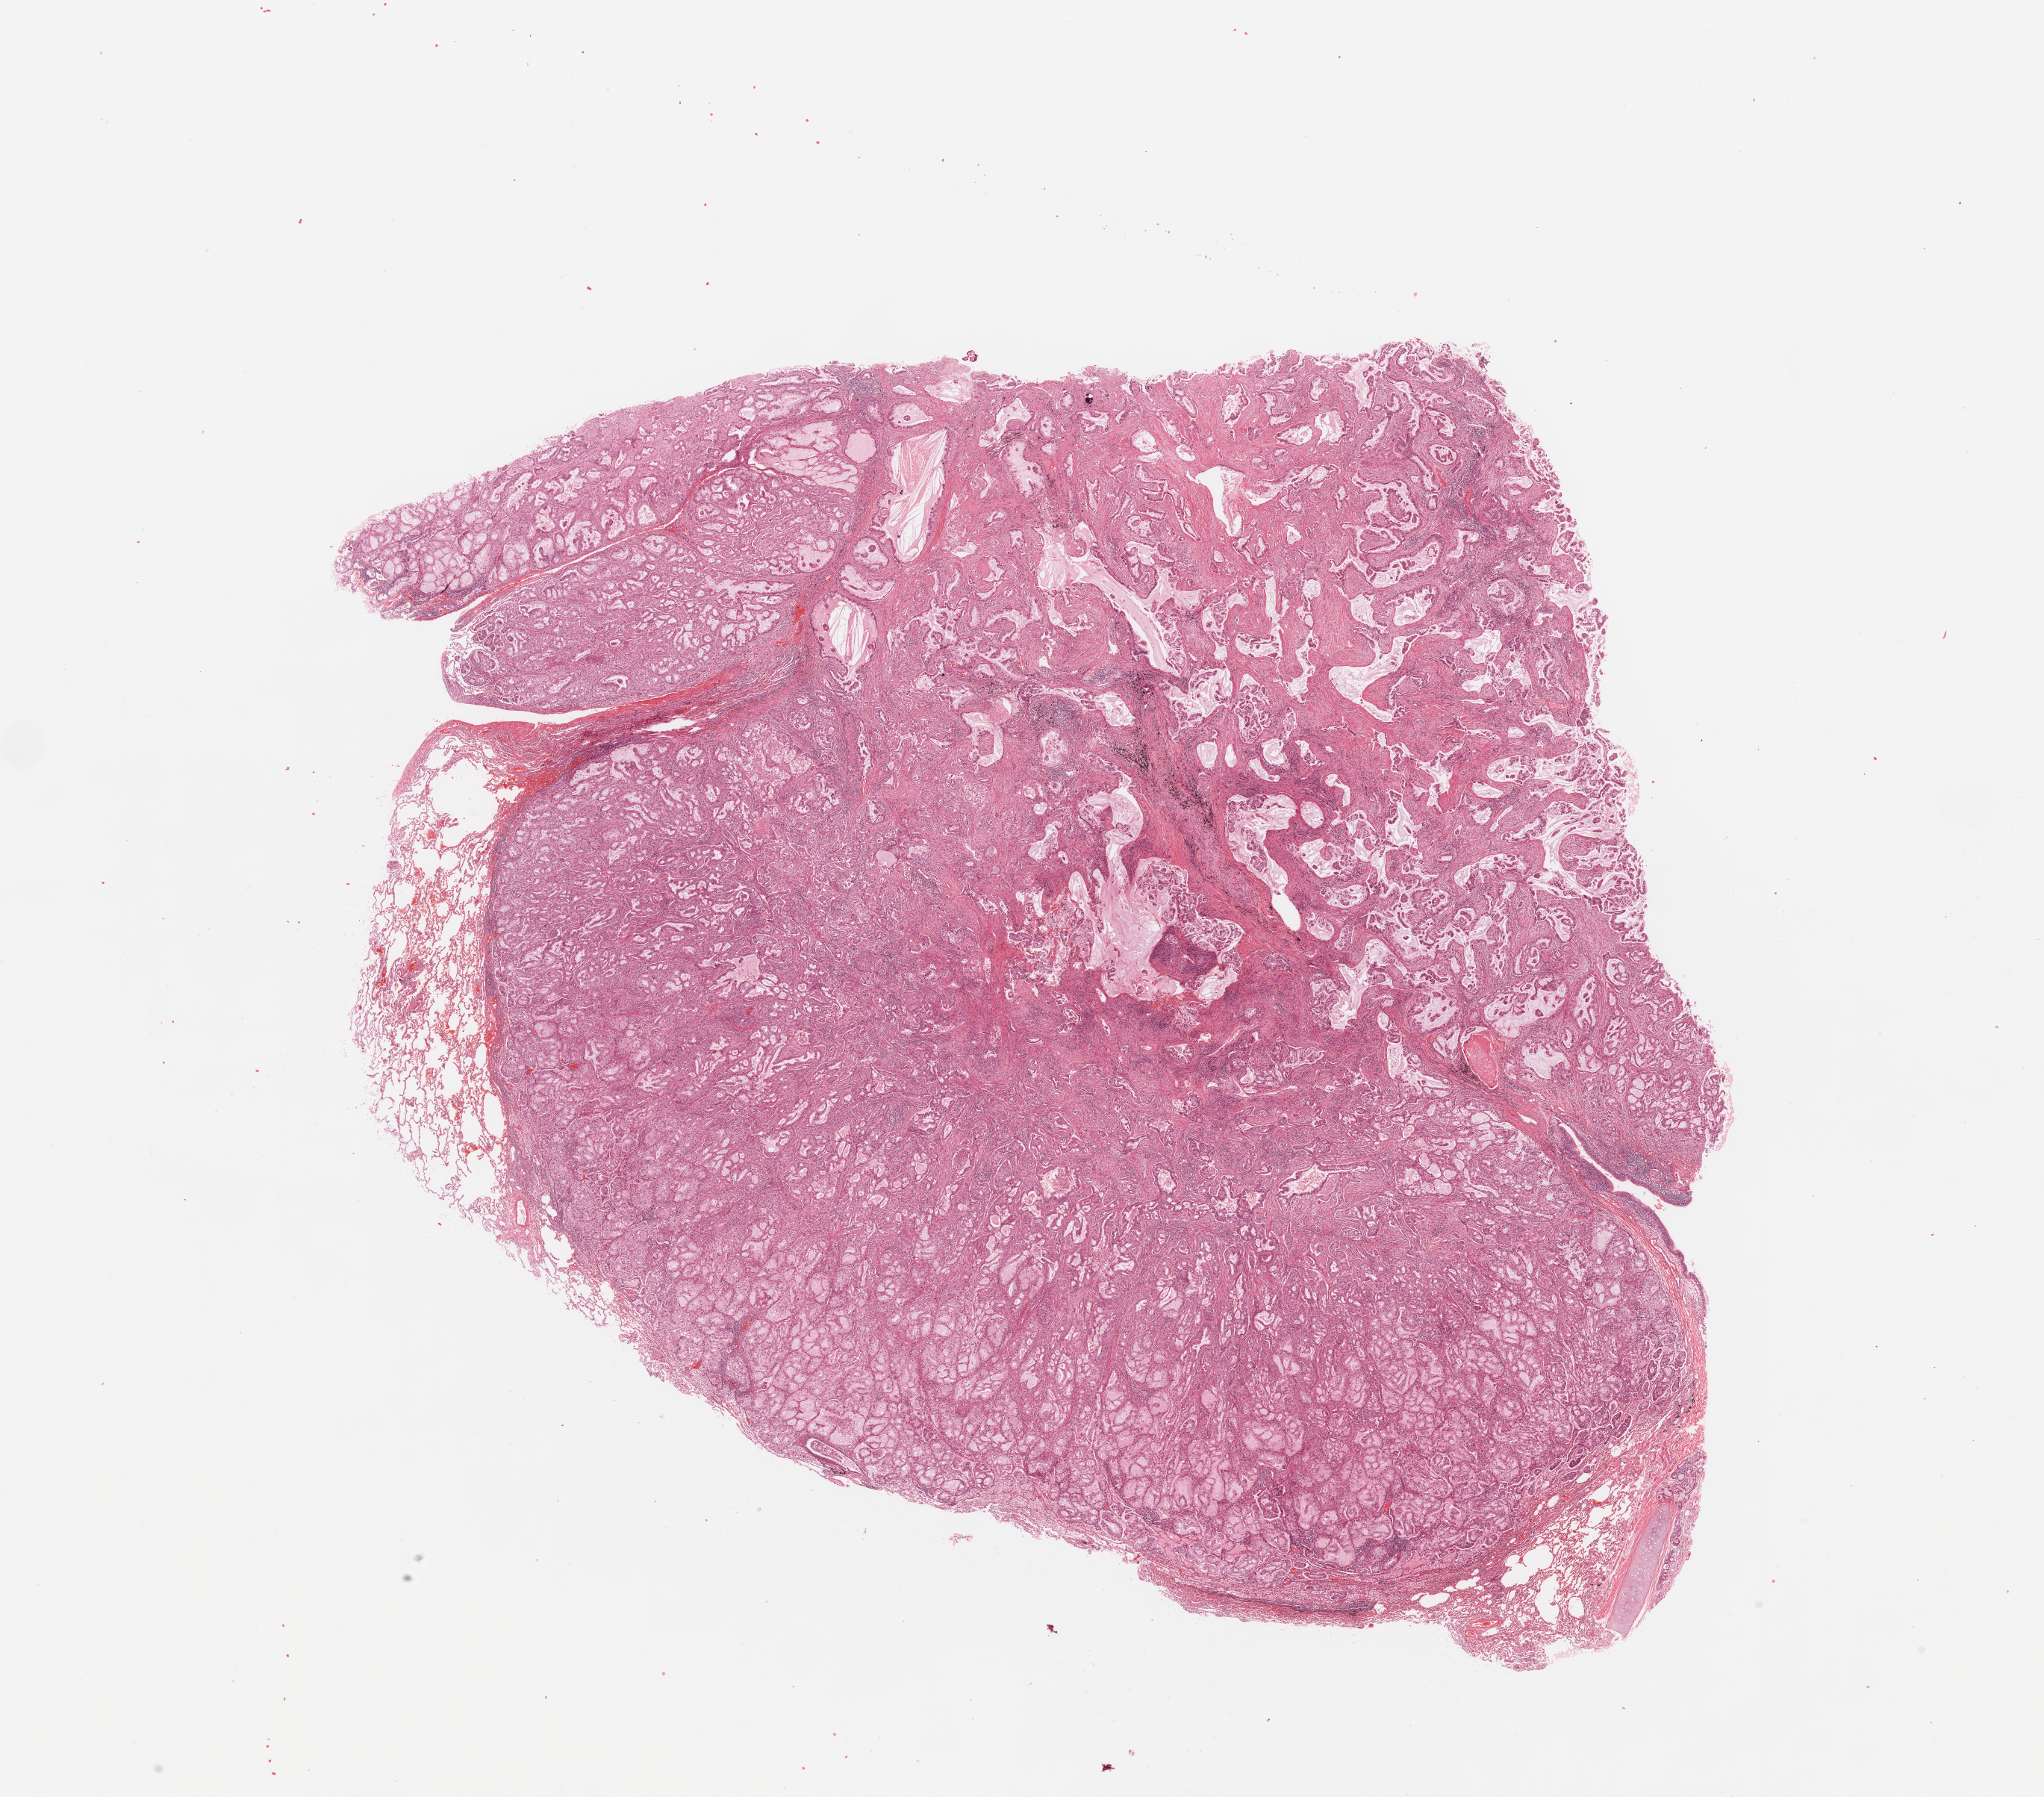
Digitized Hematoxylin and eosin (H&E) stained tissue section (whole slide), shown as a low-resolution overview of the whole scanned area (about 21.7 x 19.0 mm); tumour tissue sample, sampled site: lung. Patient: male, age 48 years. Slide review estimates, as recorded: tumour nuclei 75%, necrosis 5%.
Histologic diagnosis: Adenocarcinoma, NOS.